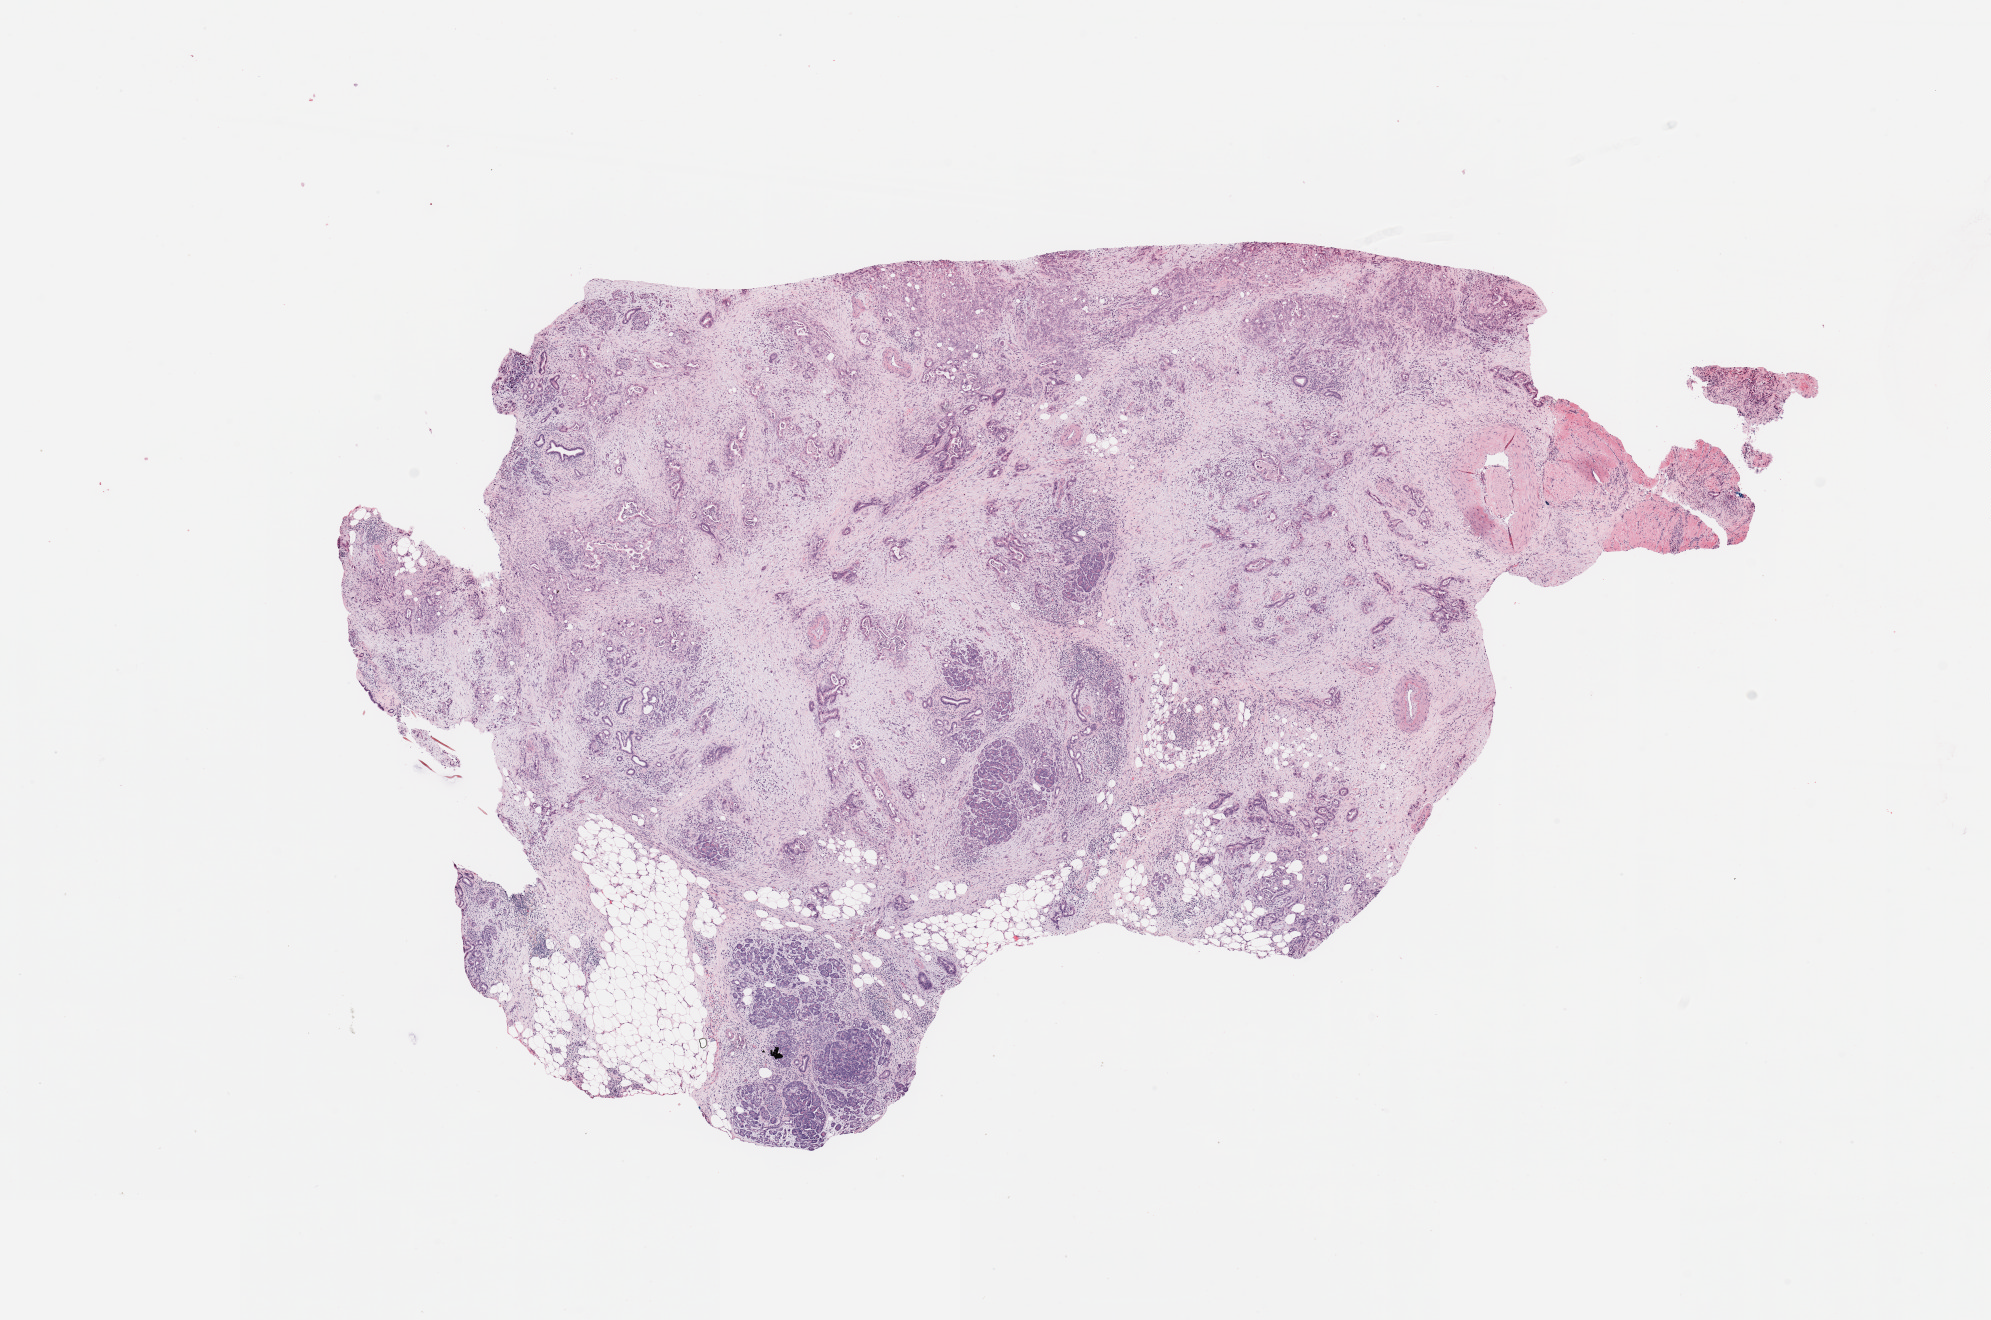
H&E-stained whole-slide image, a low-resolution overview of the entire scanned area, about 15.8 x 10.4 mm (slide scanned at 20x). Tumour tissue sample, pancreas. Female, 73 y/o. Histologic grade: G2 (moderately differentiated).
Primary tumour site (as recorded): head. Histologic diagnosis: Infiltrating duct carcinoma, NOS.